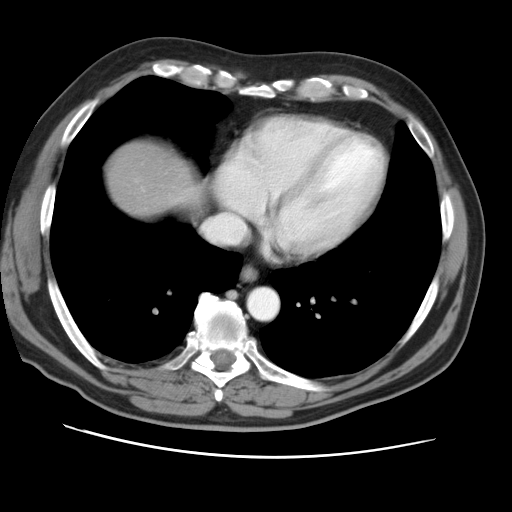
Contrast-enhanced abdominal CT, one axial slice; position 47 of 49 along the scan axis; reconstruction kernel STANDARD; intravenous contrast given; soft-tissue window (W 400 / L 40 HU); 5 mm slice thickness; 512 × 512 image matrix, field of view 374 × 374 mm. Male patient, age 59 years. Case-level facts recorded for this patient, not image findings: diagnosis: colorectal cancer liver metastases, imaged before liver resection; multiple liver metastases: yes; largest metastasis: 6.3 cm; disease in both lobes: yes.
Outlined on this slice (expert manual segmentation):
- liver: box from (x=109, y=145) to (x=196, y=214) px
- planned liver remnant (the part of the liver to remain after resection): (x=109, y=145)–(x=196, y=215)